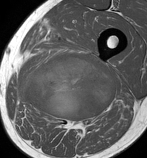
MRI of an extremity soft-tissue mass, one axial slice; position 62 of 86 along the scan axis; MR volume resampled by the dataset authors to the PET/CT grid (not the native acquisition matrix); 147 × 158 image matrix. Male patient. From the clinical record (not read from this slice): histological type: undifferentiated pleomorphic liposarcoma; grade: high; site of the primary tumour: left thigh.
Structures marked on this image (expert contour drawn on MRI and transferred to this co-registered scan by the dataset authors):
- gross tumour volume including surrounding oedema: bounding box [x1, y1, x2, y2] px = [16, 53, 115, 130]
- gross tumour volume (mass): [21, 53, 115, 121]